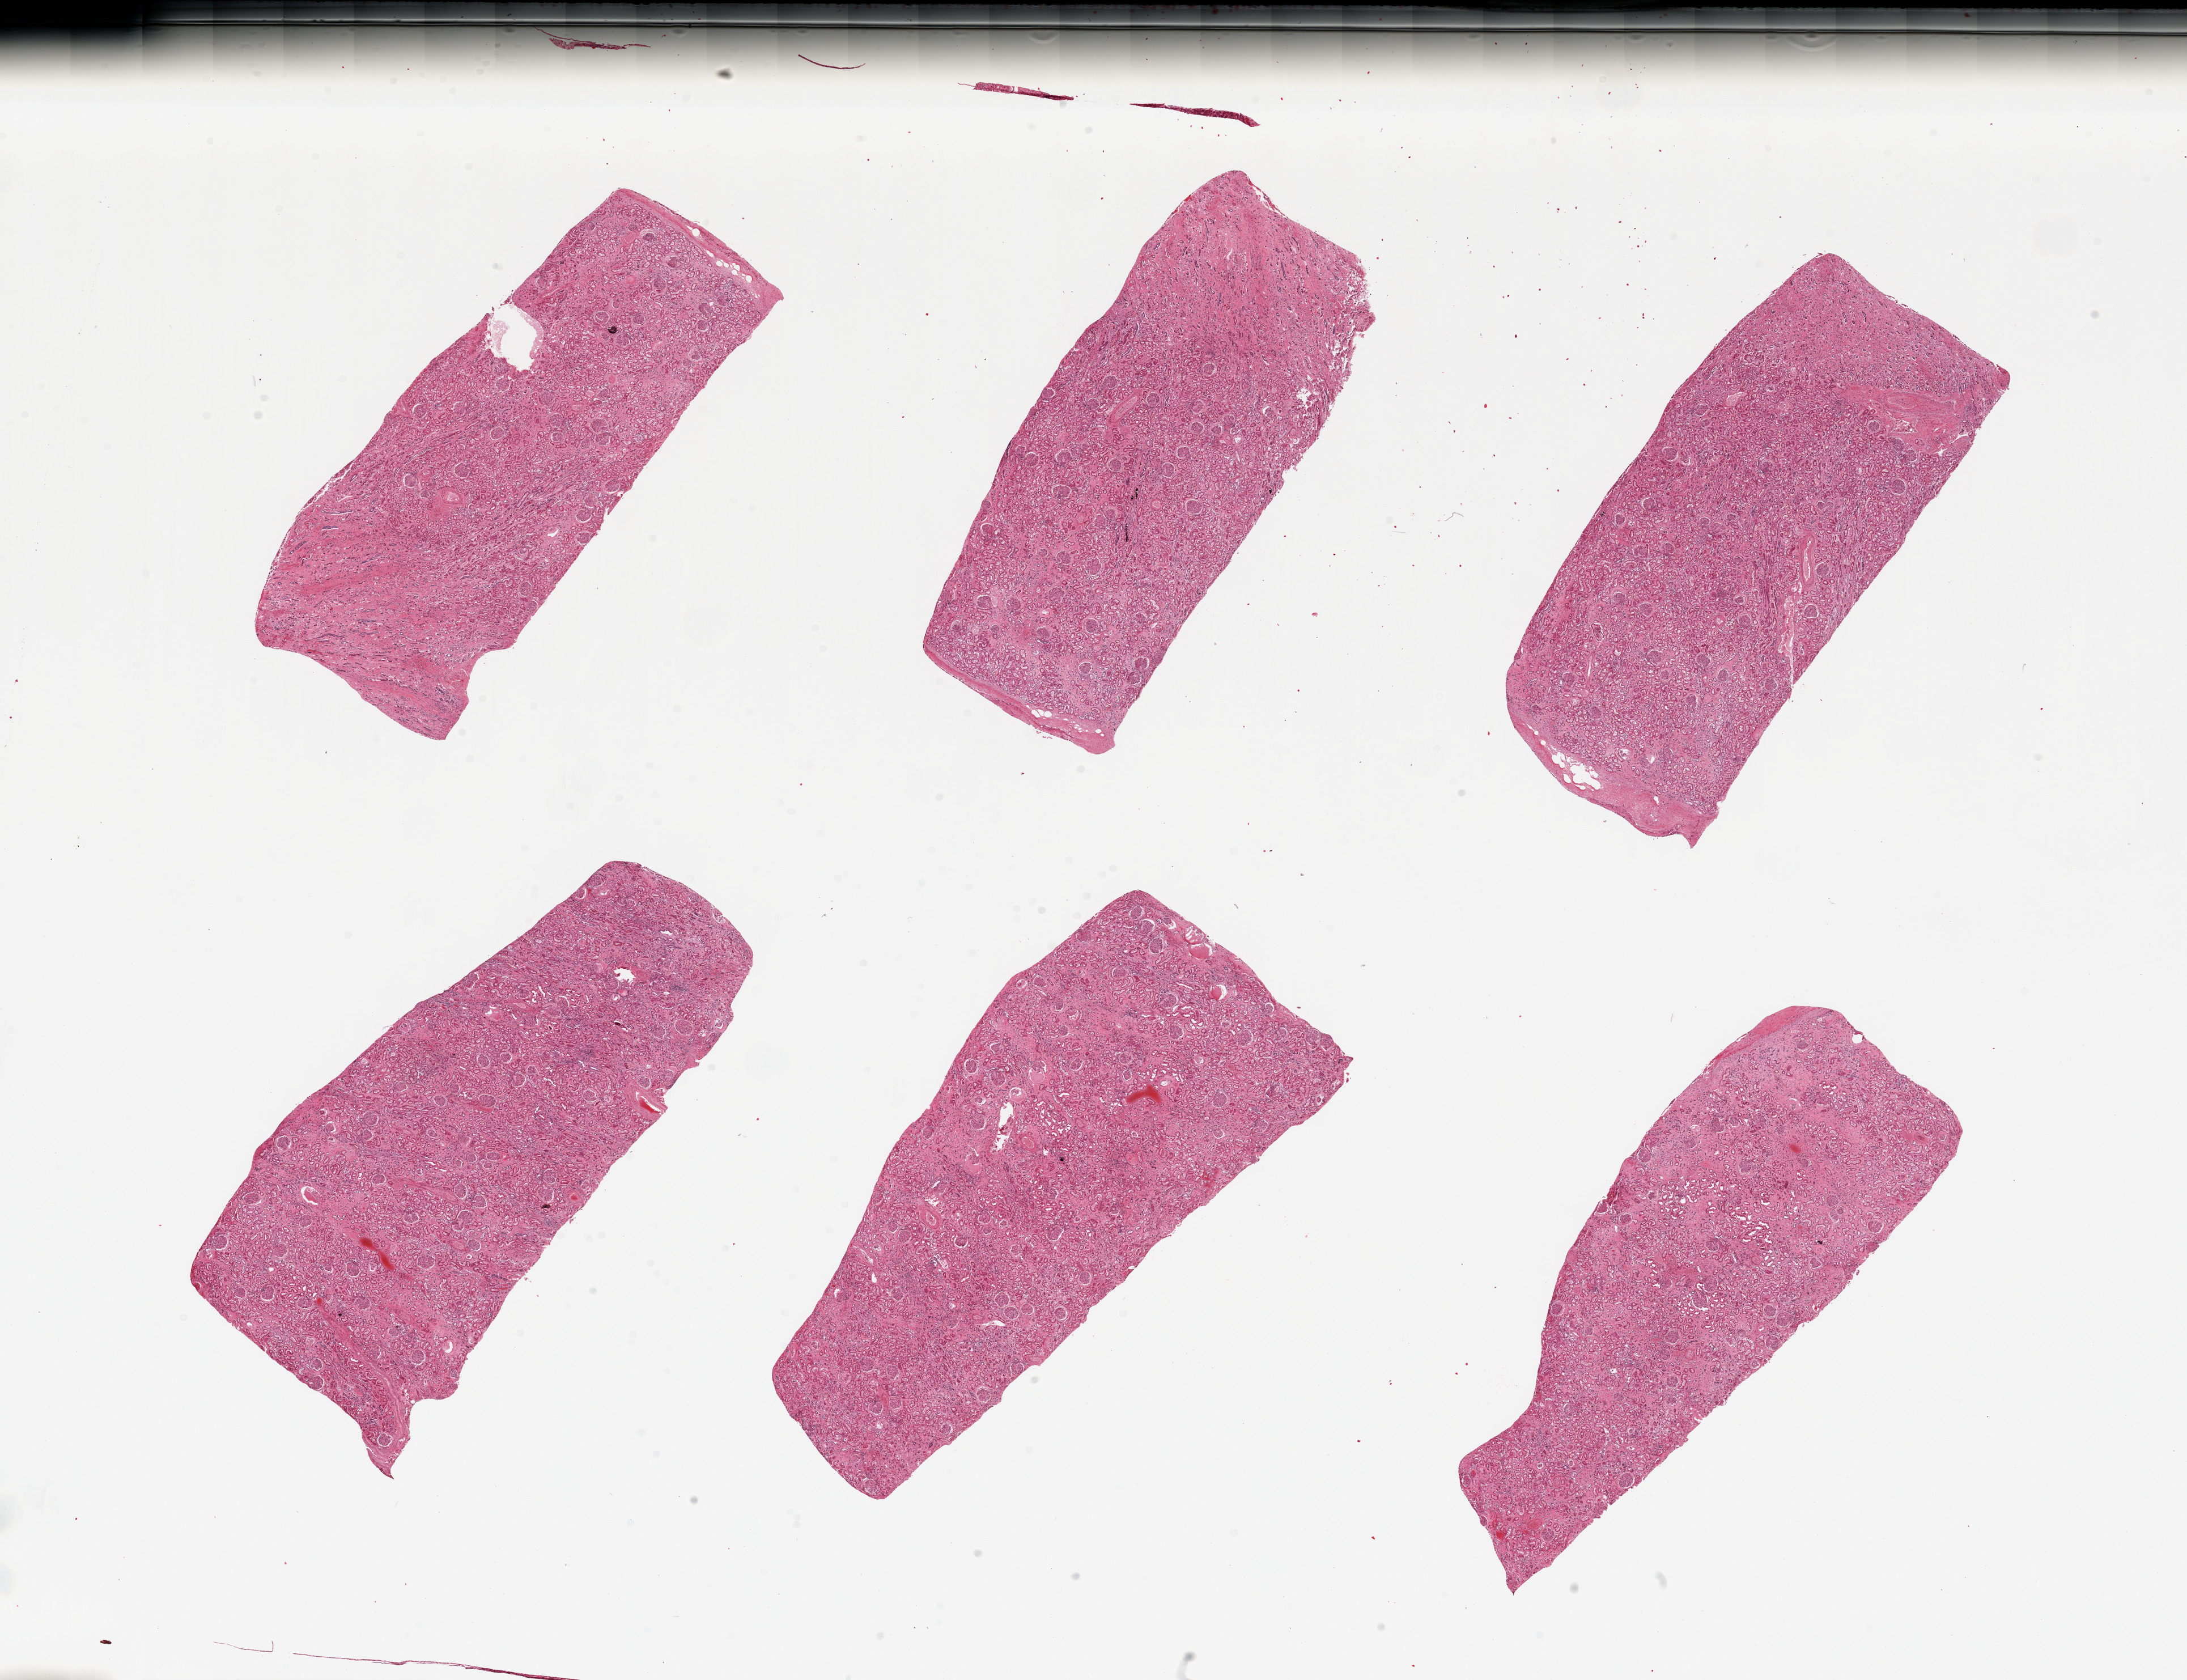
Whole-slide image, H&E stain — low-resolution overview of the scanned area, about 30.5 x 23.4 mm, PAXgene-fixed paraffin-embedded (PFPE) section, section of renal cortex (target tissue), tissue donor sample. Male donor.
Pathologist's review note for this sample: 6 pieces, glomeruli present in all pieces, moderately autolyzed tubules.